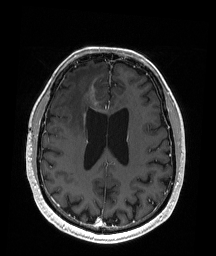
Brain MRI from a brain-tumour surgery series, one axial slice. Slice 75 of 192 in the series (ordered by position). T1-weighted post-contrast. 1 mm slice thickness. 216 × 256 image matrix, field of view 211 × 250 mm. Case-level facts recorded for this patient, not image findings: histopathology: Astrocytoma; WHO grade: 3; IDH mutation: yes; tumour location: Right Frontal.
Structures marked on this image (outlined manually by an expert reader):
- tumour: bounding box <91,92,96,105> (left, top, right, bottom; pixels)